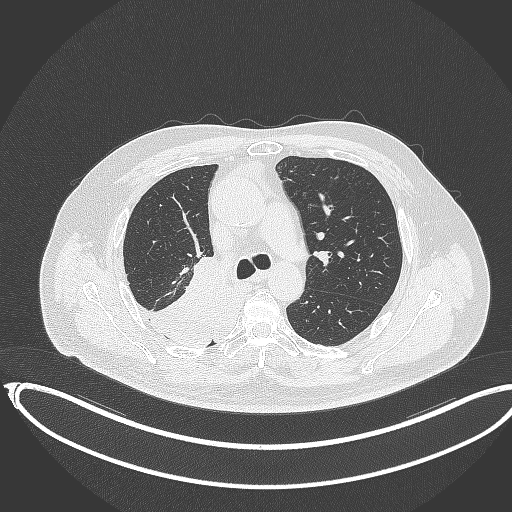
Chest CT, one axial slice; position 238 of 403 along the scan axis; 120 kVp; lung window (W 1500 / L -600 HU); 1 mm slice thickness; 512 × 512 image matrix, field of view 436 × 436 mm. Male patient, age 68 years. From the clinical record (not read from this slice): clinical TNM (as recorded): T2a N0 M0.
Structures marked on this image (rectangle marked by the reading radiologist):
- lung tumour (recorded histology: adenocarcinoma): bounding box [x1, y1, x2, y2] px = [128, 255, 227, 347]